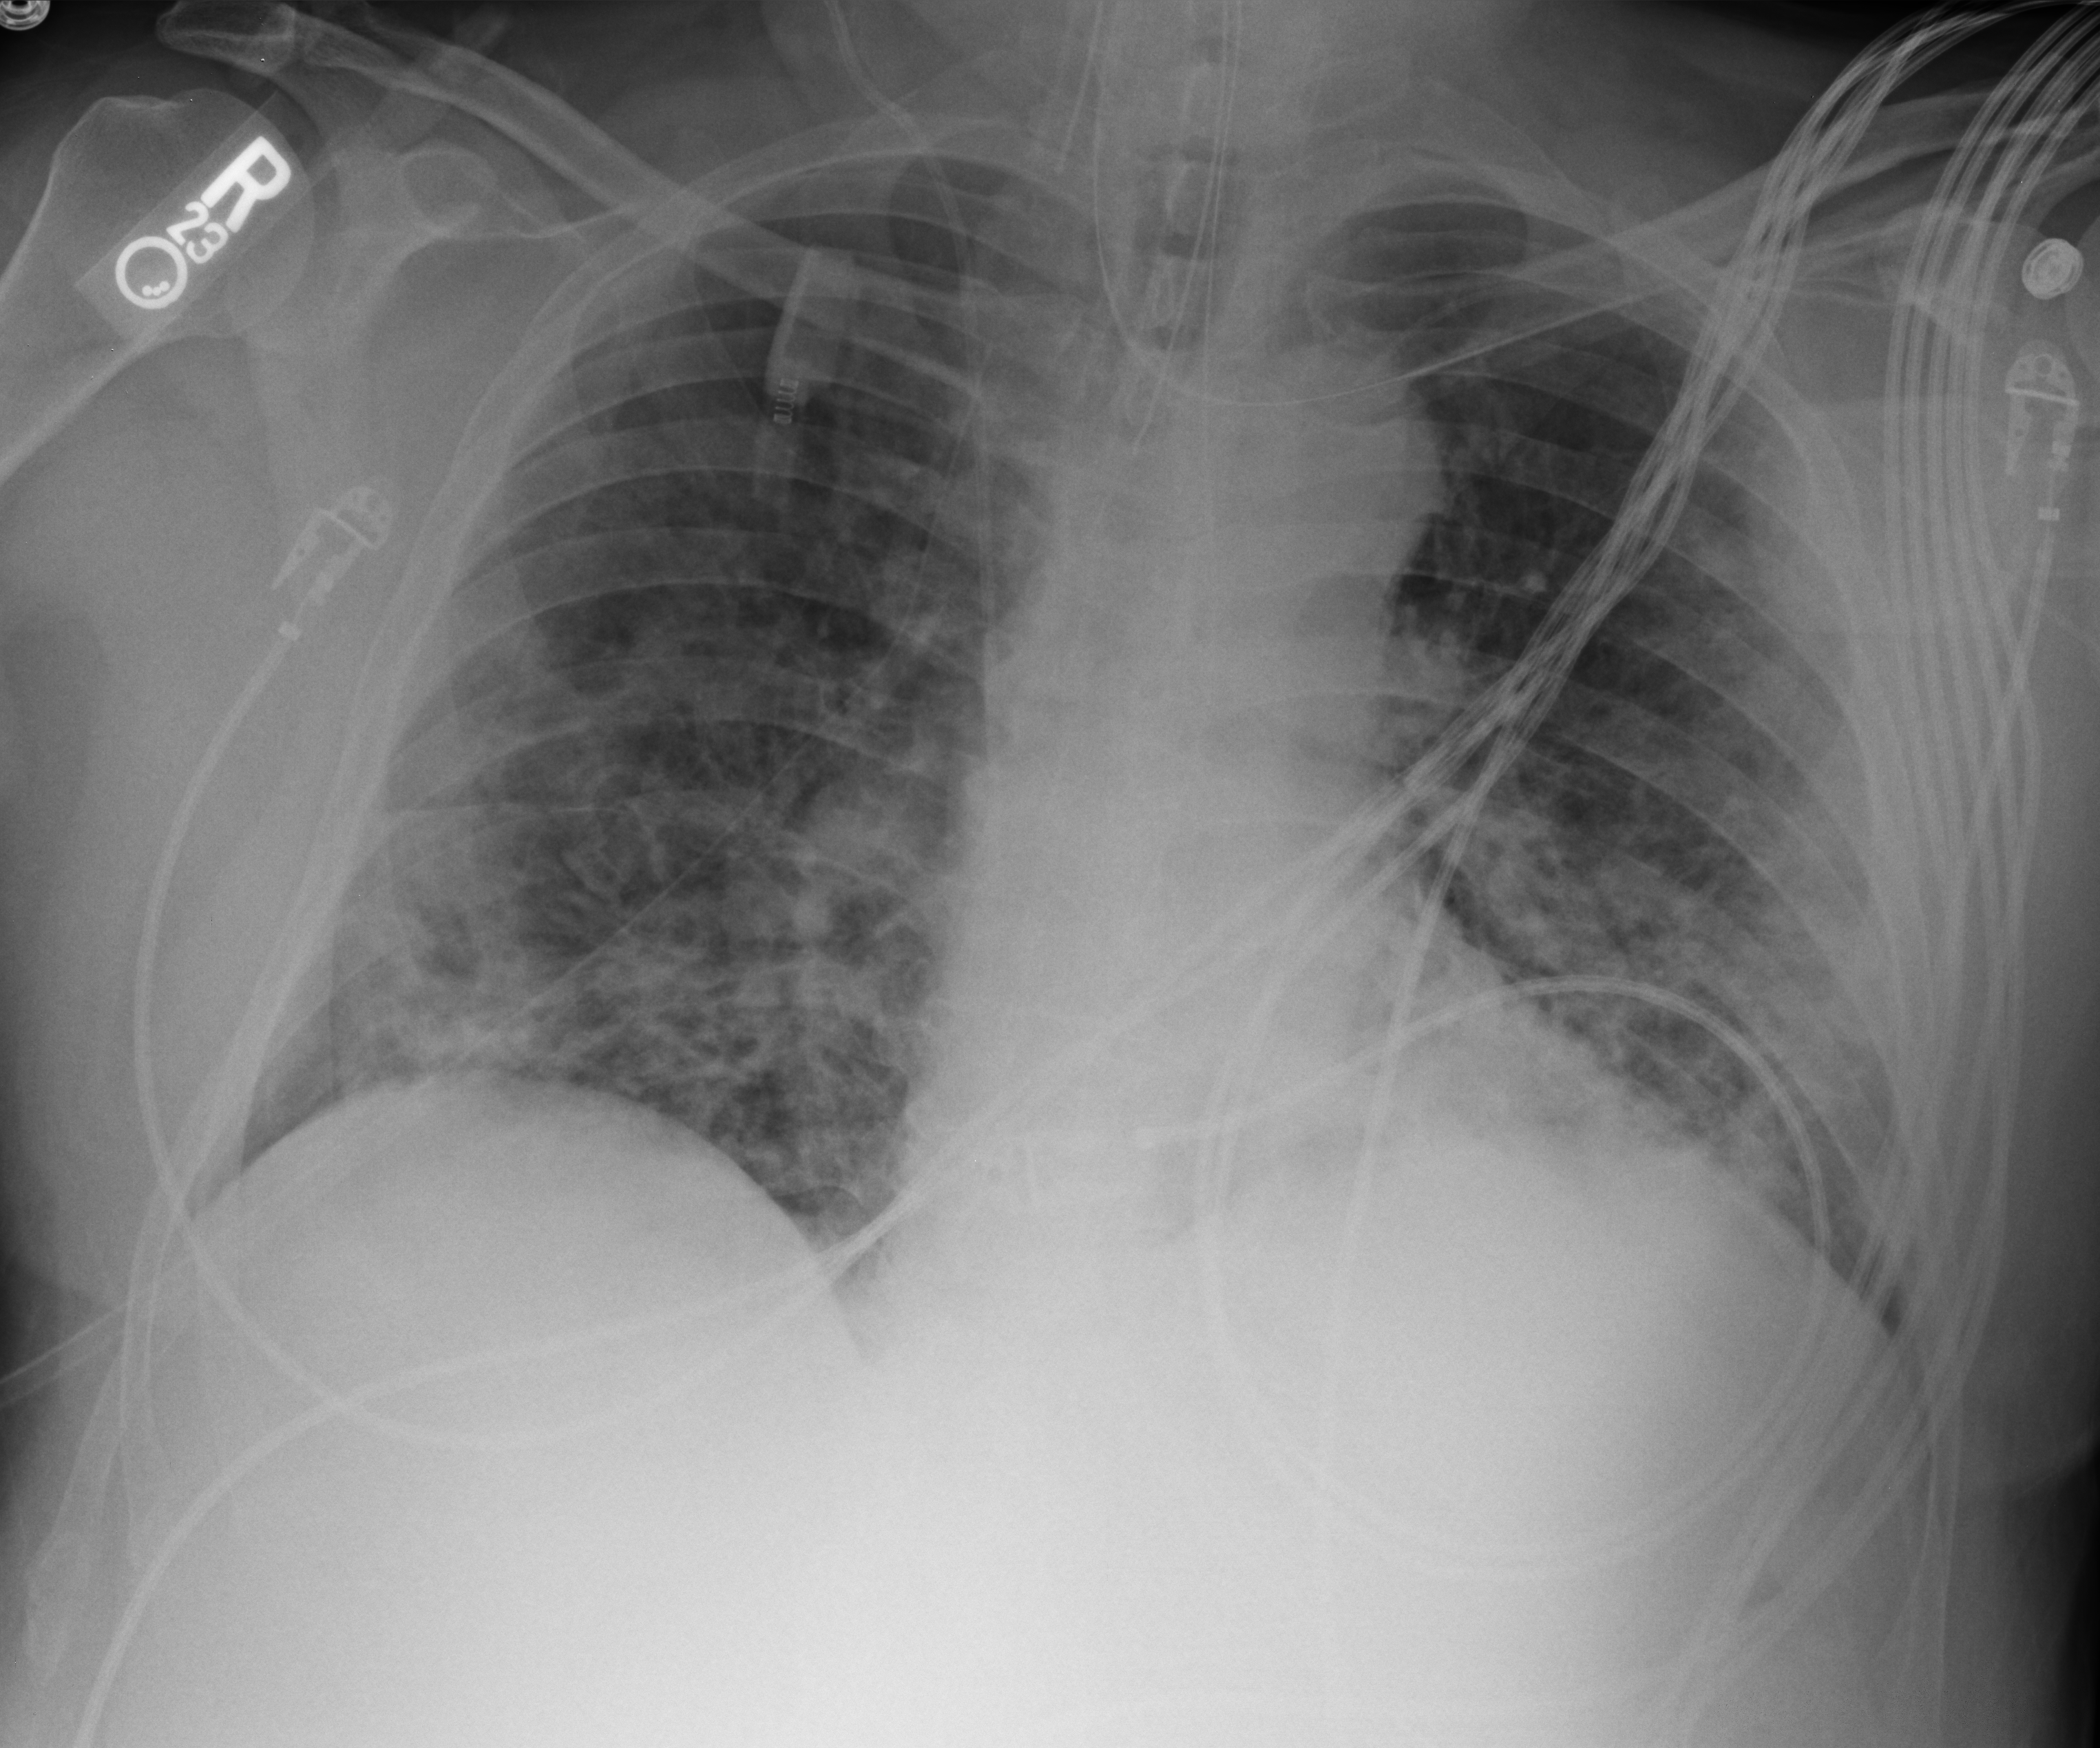
Bedside chest radiograph (computed radiography), anteroposterior (AP) projection. Patient hospitalised with COVID-19; male, aged 60–74 years.
Admission-level facts for this patient (not findings on this image; timing relative to this image not recorded): admitted to intensive care during this hospital stay: yes; hypertension (admission record): yes.